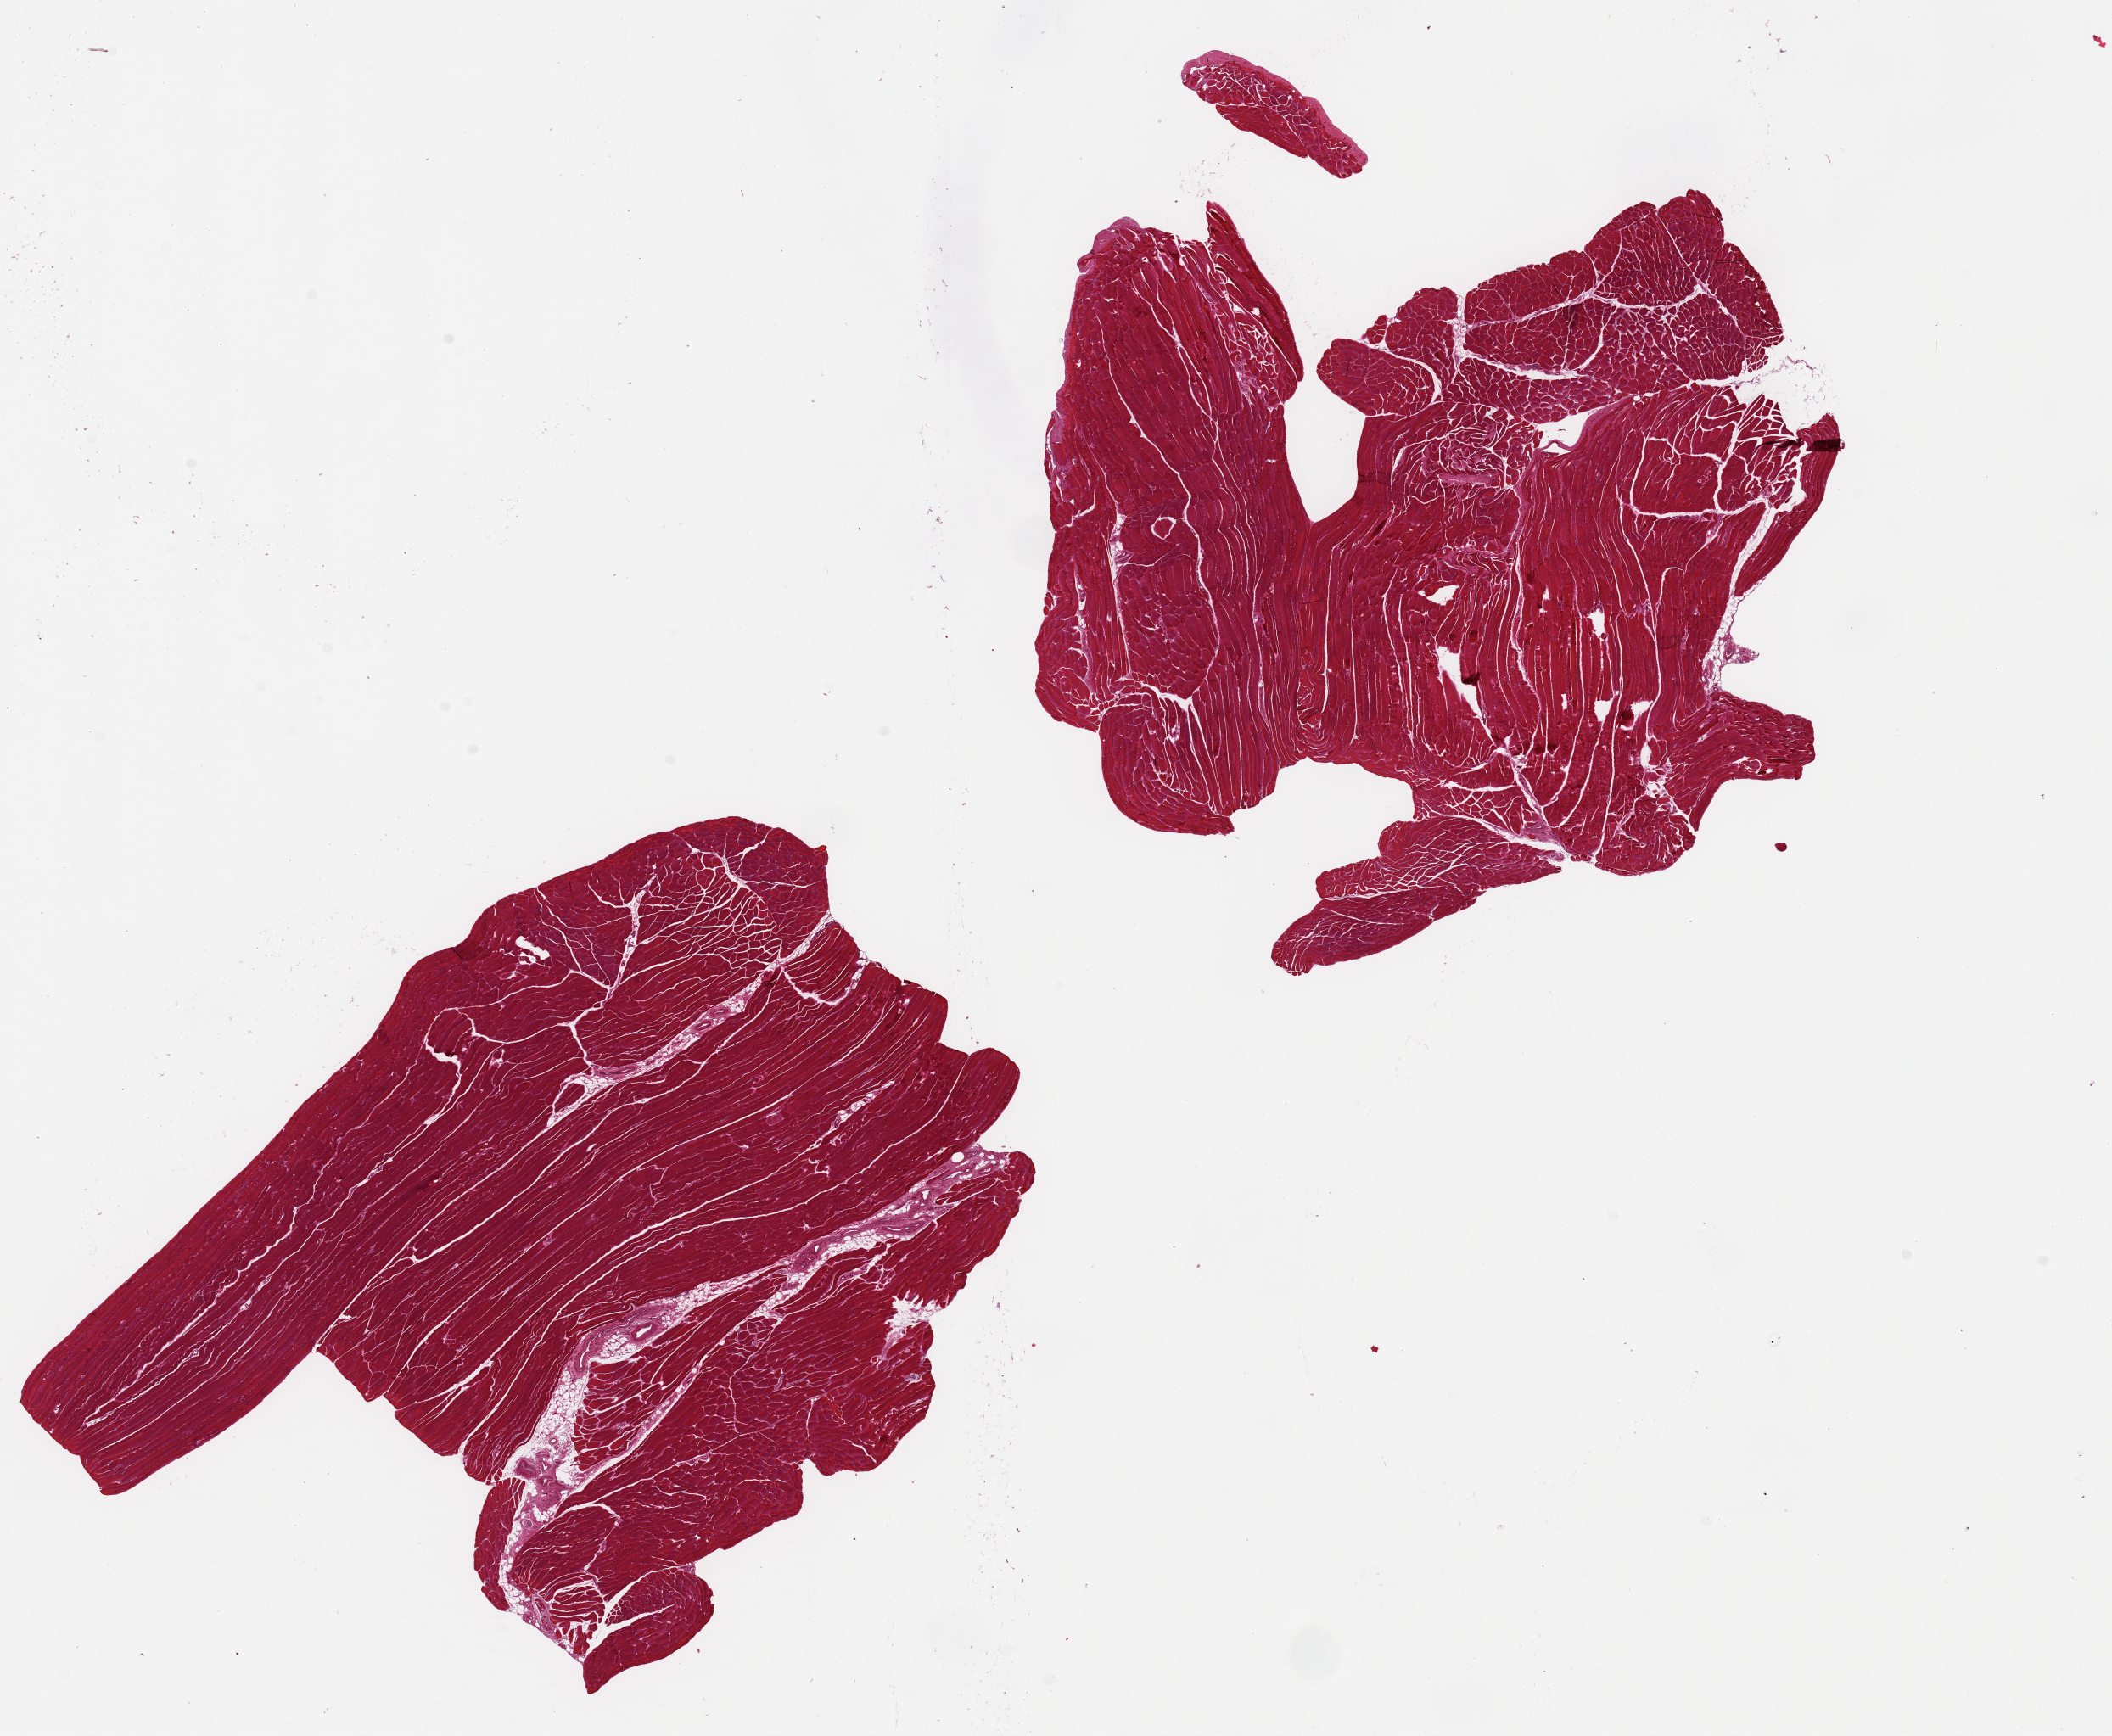
Whole-slide image, H&E stain, brightfield, a low-resolution overview of the entire scanned area, about 19.7 x 16.2 mm (acquisition: 20x scan). PAXgene-fixed, paraffin-embedded tissue. Sampled site (target tissue): skeletal muscle. Tissue donor sample. Female donor.
* review note (as recorded): 2 pieces ~8x7mm, minimal interstitial fat